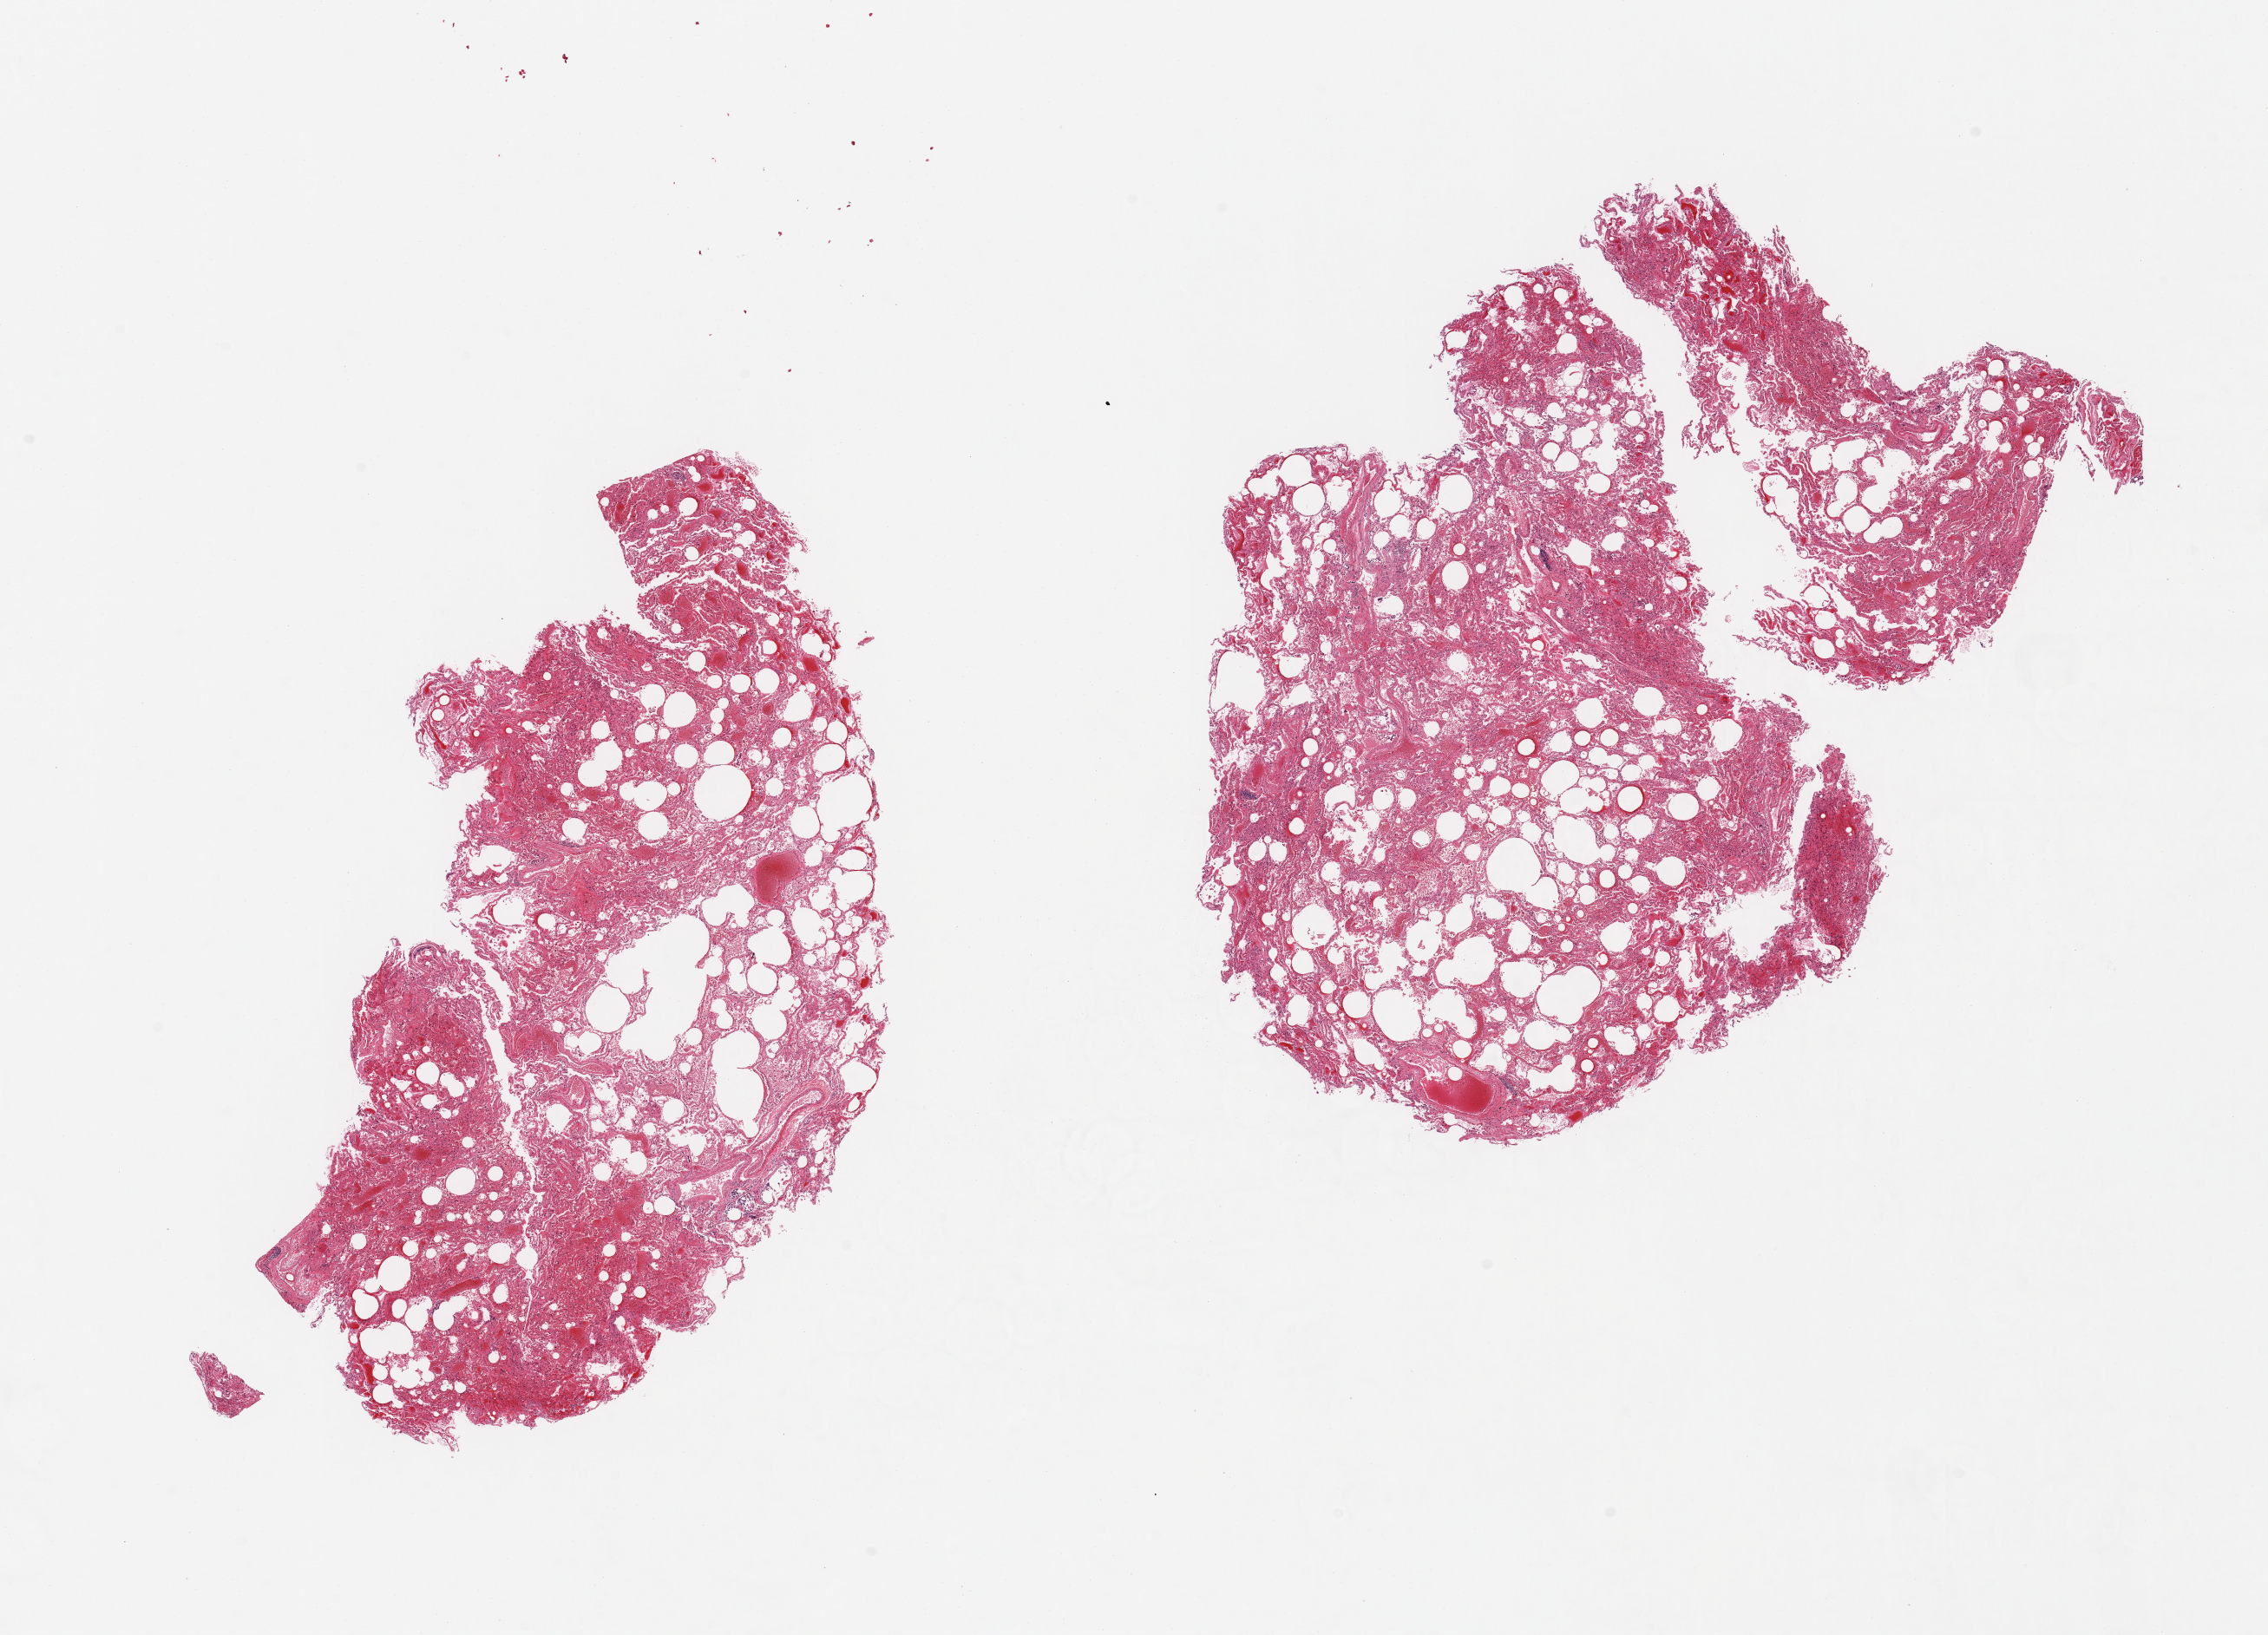
Hematoxylin and eosin (H&E) whole-slide image, a low-resolution overview of the entire scanned area, about 20.7 x 14.9 mm, PAXgene-fixed paraffin-embedded (PFPE) section, target tissue: lung, donor tissue sample. Donor: female.
- reviewer comment on this tissue sample: 2 pieces; moderate vascular congestion and focal edema